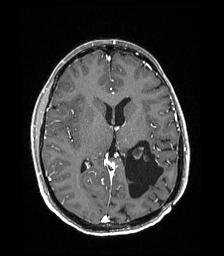
Brain MRI from a brain-tumour surgery series, one axial slice. T1-weighted post-contrast. 1 mm slice thickness. 224 × 256 image matrix, field of view 224 × 256 mm. From the clinical record (not read from this slice): histopathology: Low grade glioma; IDH mutation: no.
Outlined on this slice (outlined manually by an expert reader):
- previous resection cavity: bounding box <125,140,163,203> (left, top, right, bottom; pixels)
- tumour: <132,146,147,159>